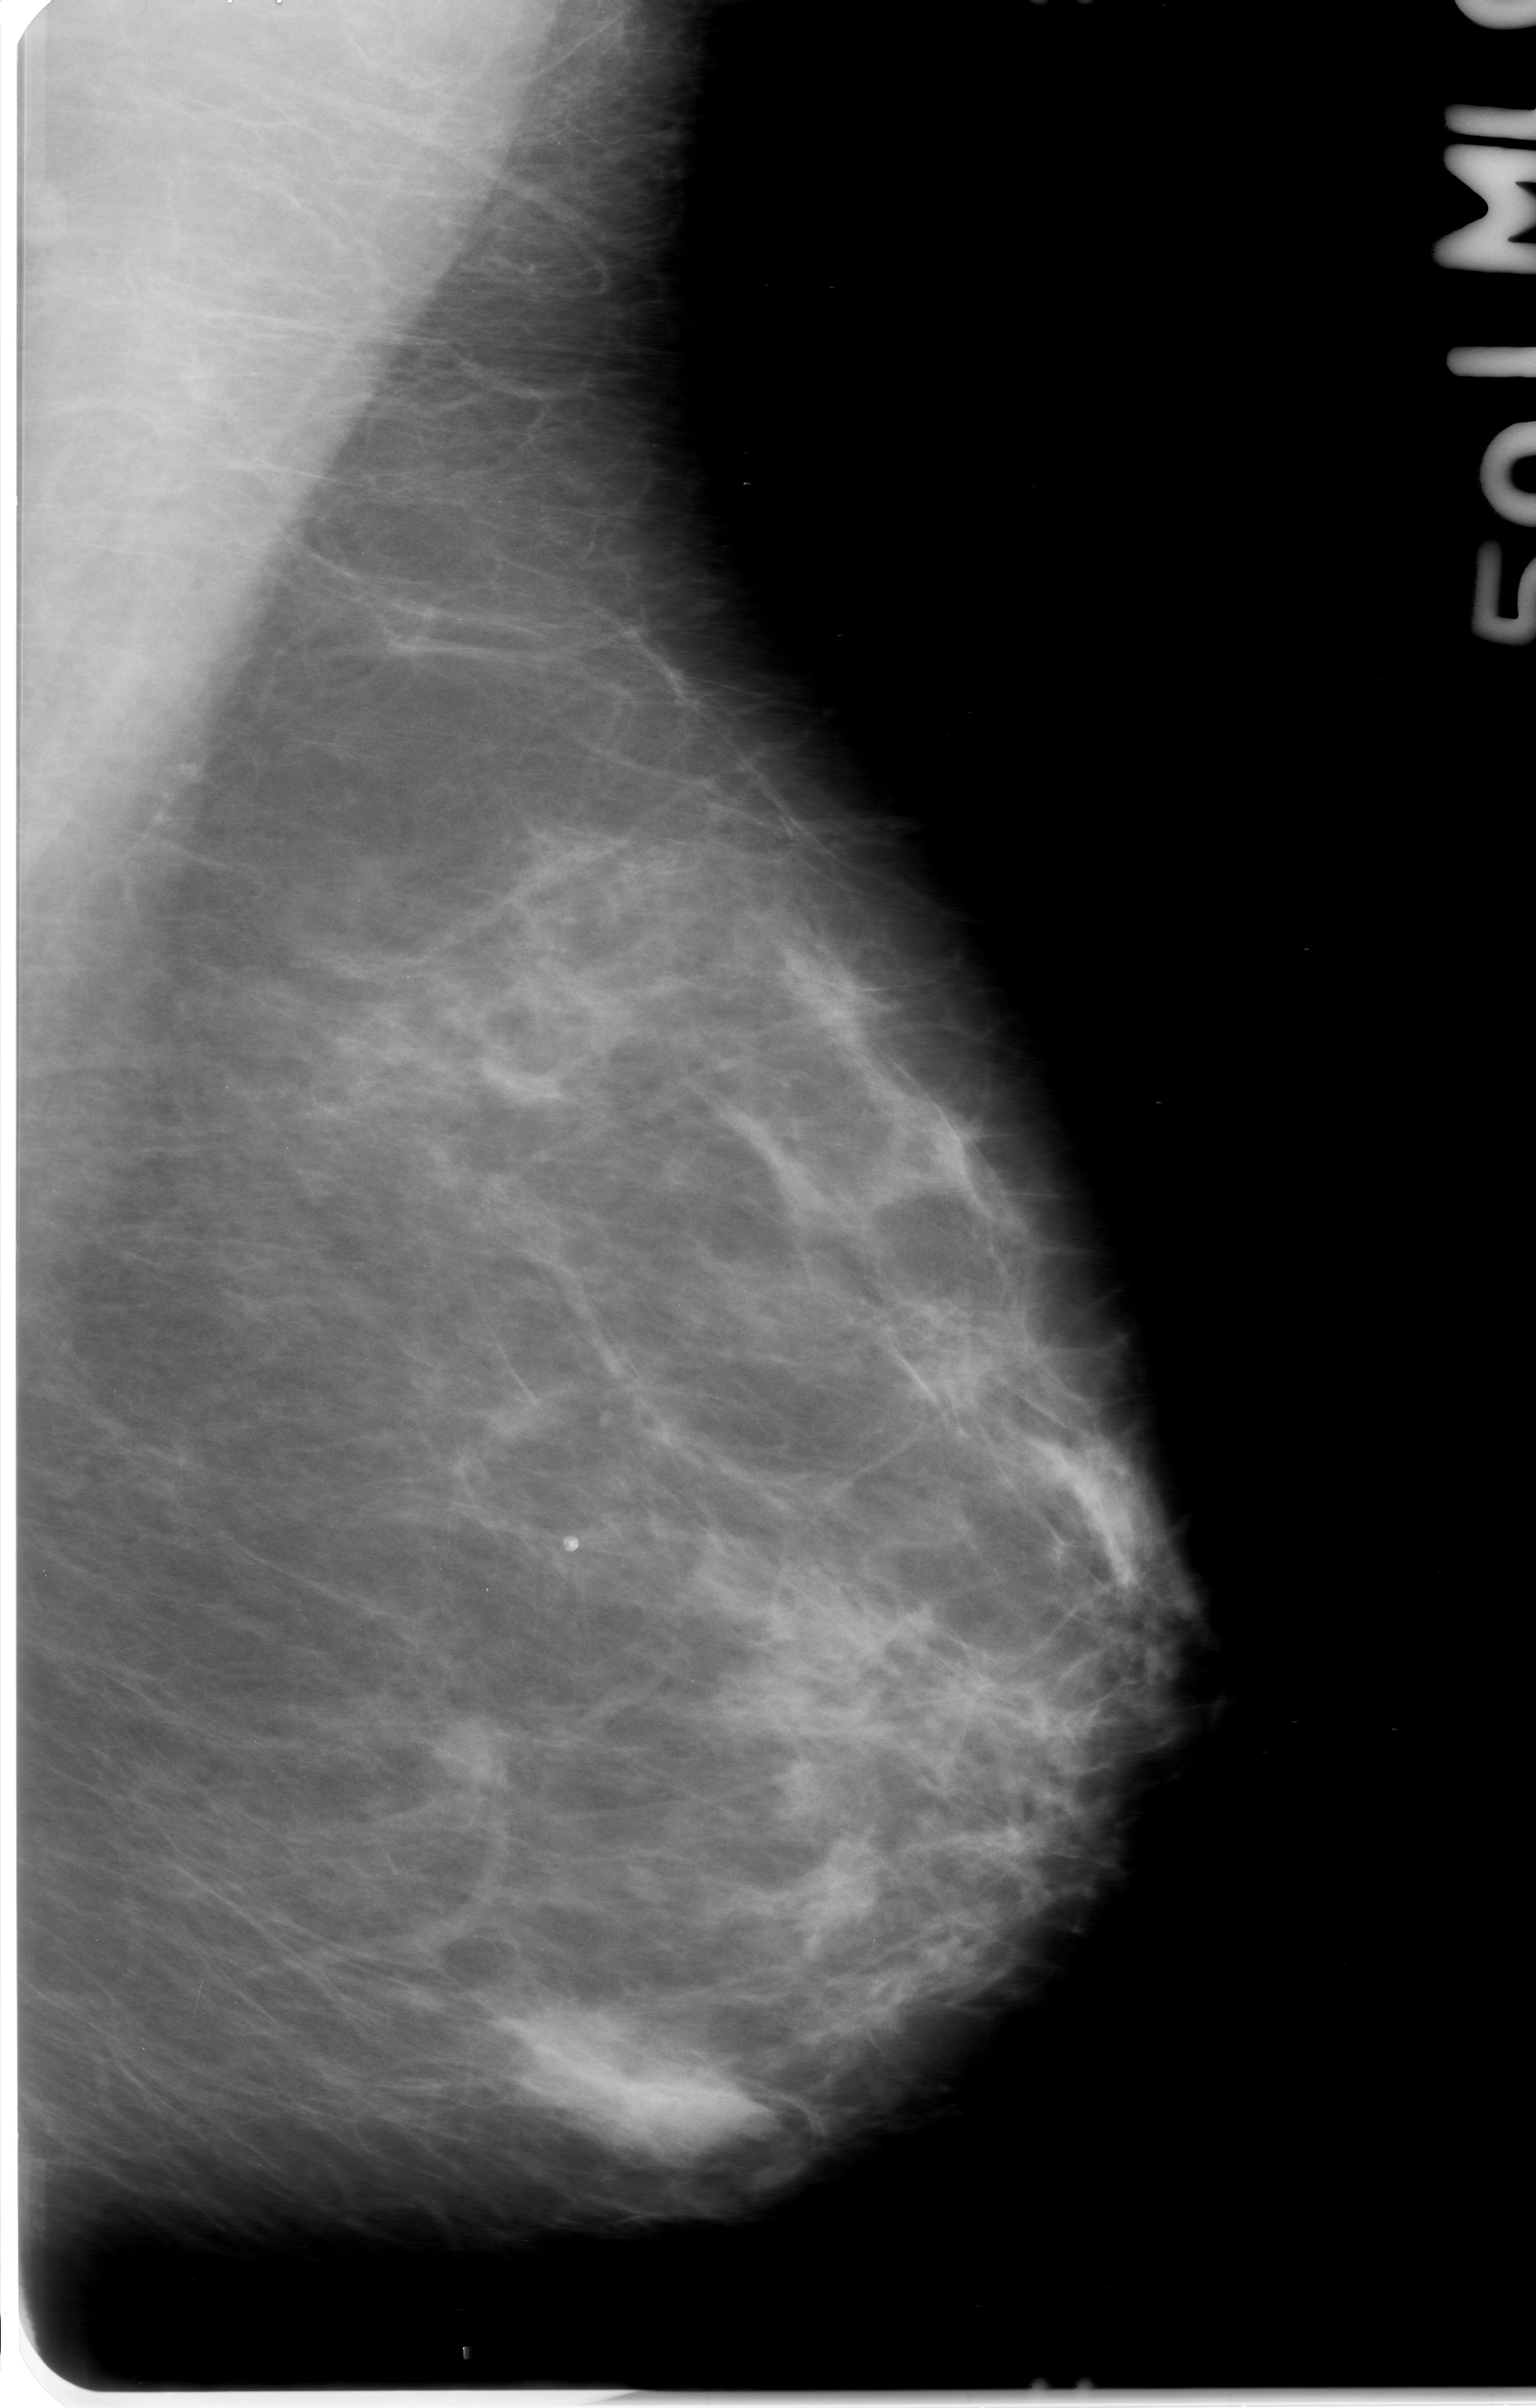
Digitized screen-film mammogram; left breast; MLO view.
Finding: mass, shape oval, margins obscured; BI-RADS assessment category 0 (incomplete: needs additional imaging); subtlety rating 4 on a 1 (subtle) to 5 (obvious) scale; pathology result (as recorded, not read from the image): benign.